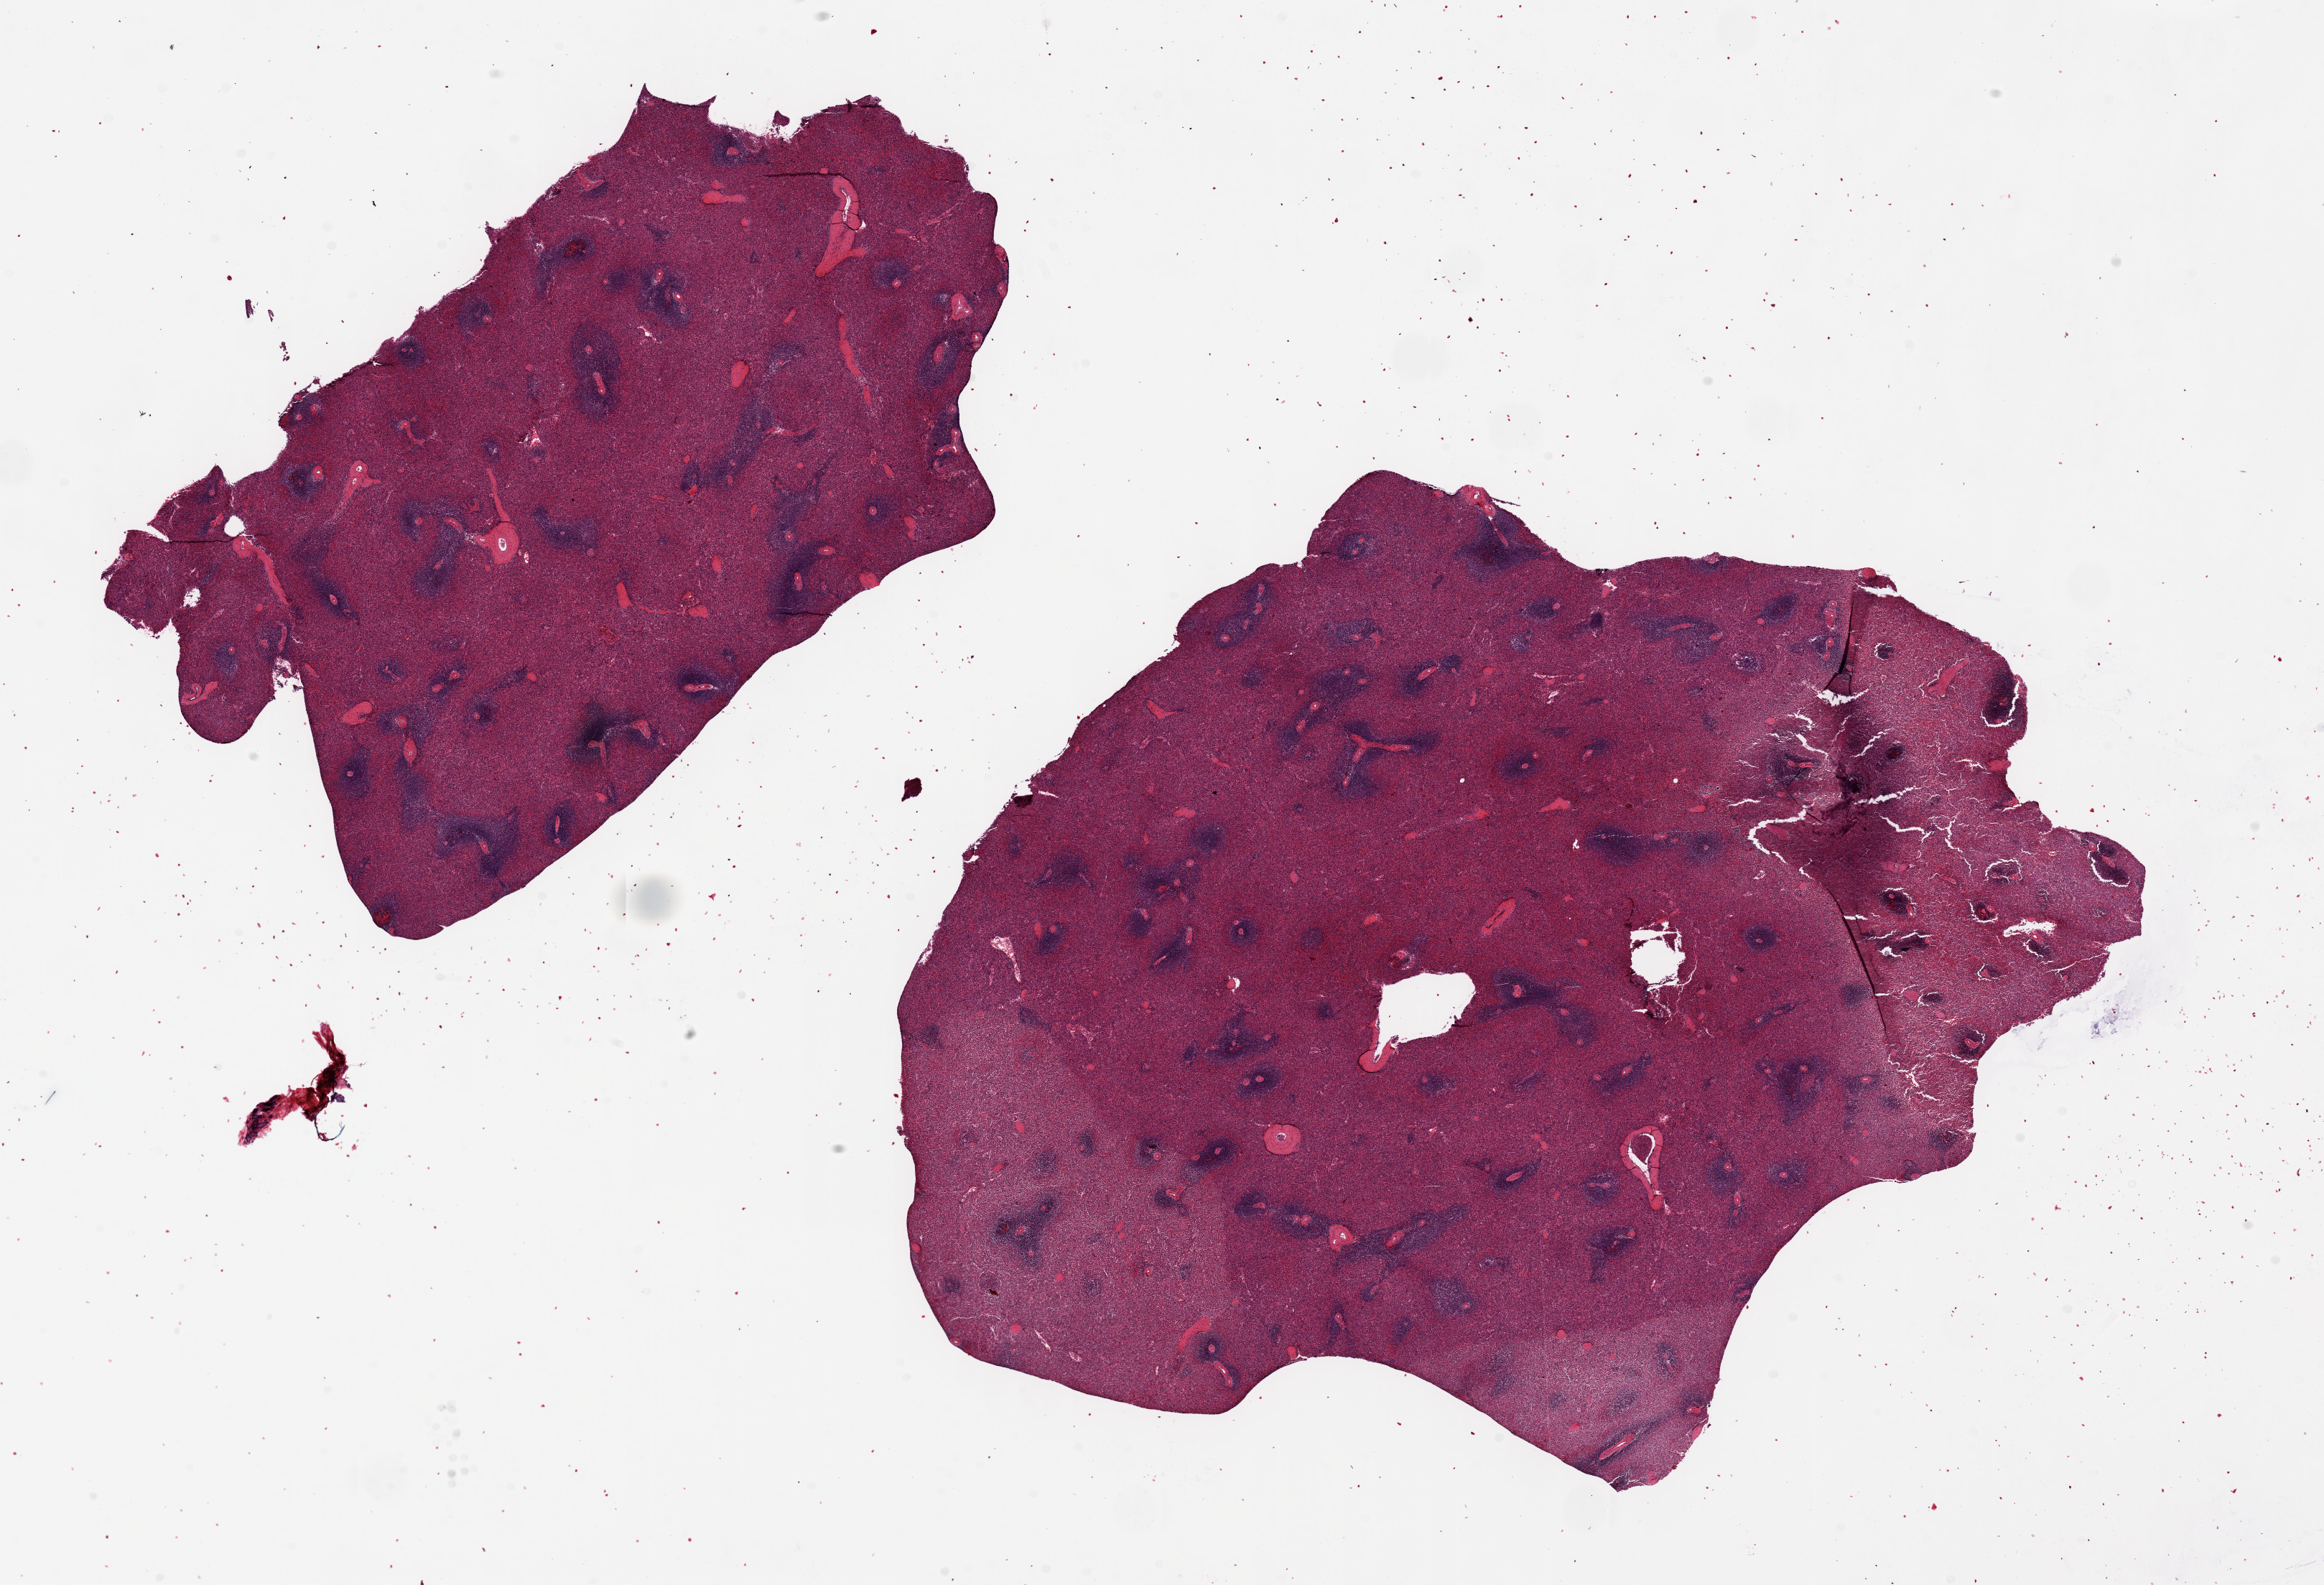
Digitized hematoxylin and eosin (H&E)-stained section, whole scanned area (about 25.6 x 17.5 mm) shown as a low-resolution overview, PAXgene-fixed, paraffin-embedded tissue, section of spleen (target tissue), donor tissue sample. Donor: male.
Reviewer comment on this tissue sample: 2 pieces ~10x8. Well preserved.